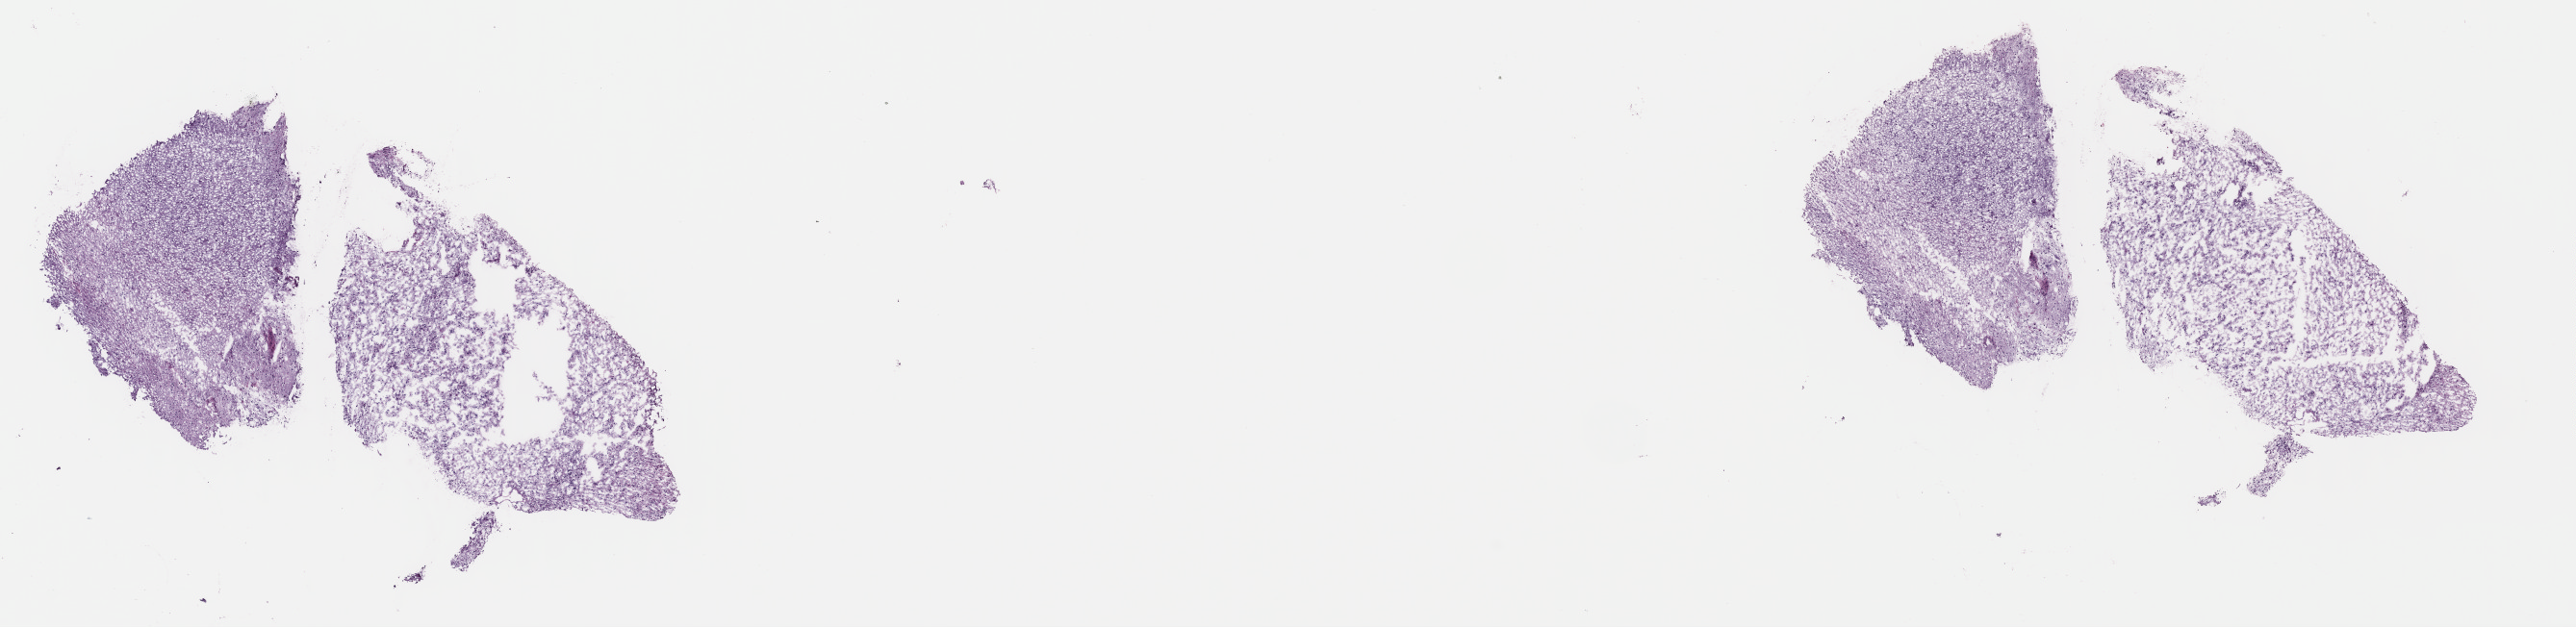
Whole-slide histology image, H&E, shown as a low-resolution overview of the whole scanned area (about 21.0 x 5.1 mm, from a 40x scan); frozen section; primary tumour sample from the brain. Male, age 33 years at initial diagnosis. Histologic grade: G2 (moderately differentiated). Pathologist review of this section (percent, as recorded): tumour cells 30%, tumour nuclei 80%, normal cells 10%, stromal cells 60%, necrosis 0%. Infiltration values recorded for this section: lymphocyte infiltration 0%, monocyte infiltration 0%, neutrophil infiltration 0%.
• histologic diagnosis: Mixed glioma (cerebrum)